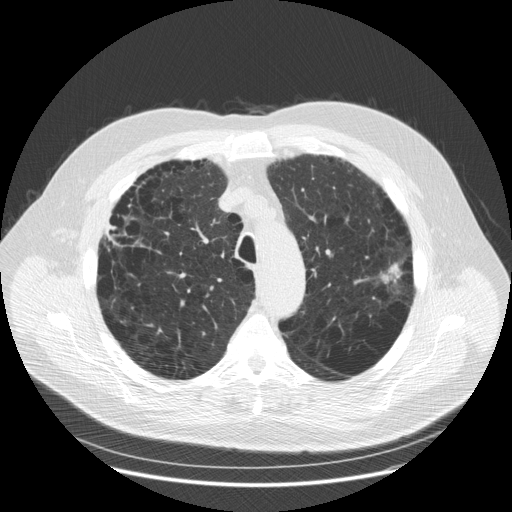
Low-dose screening chest CT, one axial slice; position 134 of 179 along the scan axis; reconstruction kernel STANDARD; 120 kVp; lung window (W 1500 / L -600 HU); 2.5 mm slice thickness; 512 × 512 image matrix, field of view 404 × 404 mm.
Outlined on this slice (expert manual segmentation):
- lesion 1 (tumor, upper lobe of left lung): bounding box <380,263,403,284> (left, top, right, bottom; pixels)